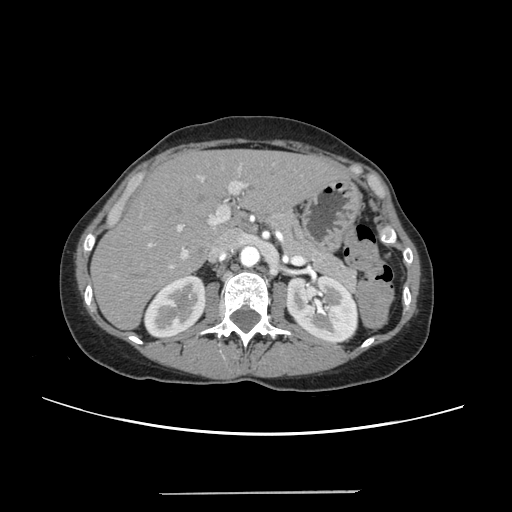
Contrast-enhanced abdominal CT, one axial slice; position 145 of 240 along the scan axis; 120 kVp; soft-tissue window (W 400 / L 40 HU); 1.25 mm slice thickness; 512 × 512 image matrix, field of view 371 × 371 mm. Female patient, age 60 years. Case-level facts recorded for this patient, not image findings: diagnosis: colorectal cancer liver metastases, imaged before liver resection; multiple liver metastases: no; largest metastasis: 1.5 cm; chemotherapy before resection: yes.
Annotated regions visible in this slice (expert manual segmentation):
- liver: bounding box [x1, y1, x2, y2] px = [93, 151, 344, 327]
- planned liver remnant (the part of the liver to remain after resection): [93, 151, 343, 327]
- portal vein (with intrahepatic branches): [144, 164, 251, 268]